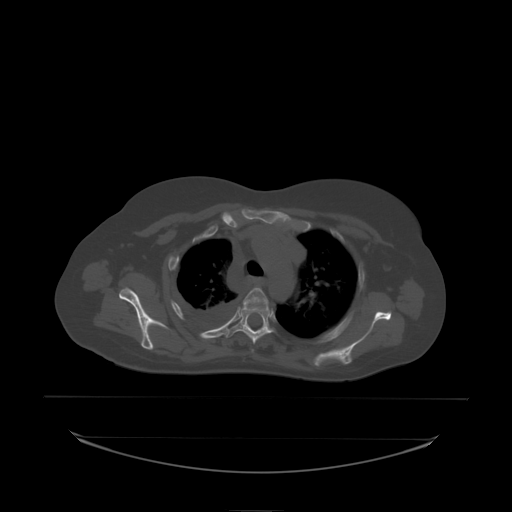
CT including the spine, one axial slice. Slice 168 of 242 in the series (ordered by position). Bone window (W 1800 / L 400 HU). 512 × 512 image matrix, field of view 500 × 500 mm. Female patient, age 53 years. Case-level facts recorded for this patient, not image findings: primary cancer: lung.
Outlined on this slice (semi-automatically segmented with operator editing):
- T3 vertebra: box from (x=243, y=288) to (x=269, y=307) px
- T4 vertebra: (x=227, y=303)–(x=275, y=338)